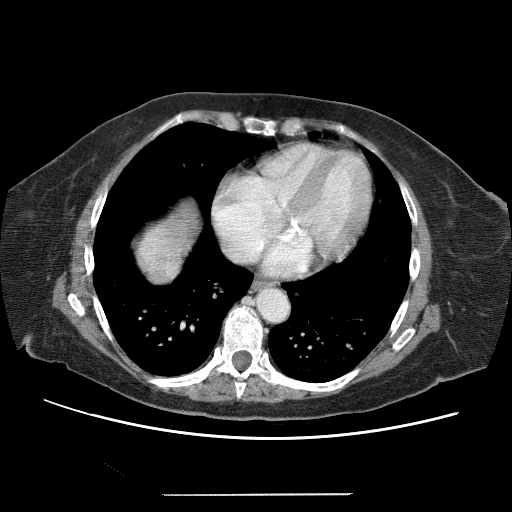
Contrast-enhanced abdominal CT (liver protocol), one axial slice; slice 62 of 65 in the series (ordered by position); 120 kVp; soft-tissue window (W 400 / L 40 HU); 512 × 512 image matrix, field of view 380 × 380 mm. Case-level facts recorded for this patient, not image findings: diagnosis: hepatocellular carcinoma (patient treated with transarterial chemoembolisation; whether this scan precedes or follows treatment is not stated here); TNM stage (as recorded): Stage-IIIB; Child-Pugh class: A; tumour differentiation: moderately differentiated; tumour nodularity: uninodular.
Structures marked on this image (semi-automatically segmented with operator editing):
- abdominal aorta: bounding box <260,291,289,323> (left, top, right, bottom; pixels)
- liver parenchyma outside the tumour (the mass and vessels are separate outlines, so this box may not span the whole liver): <144,238,170,272>
- liver vessels: <148,243,166,268>